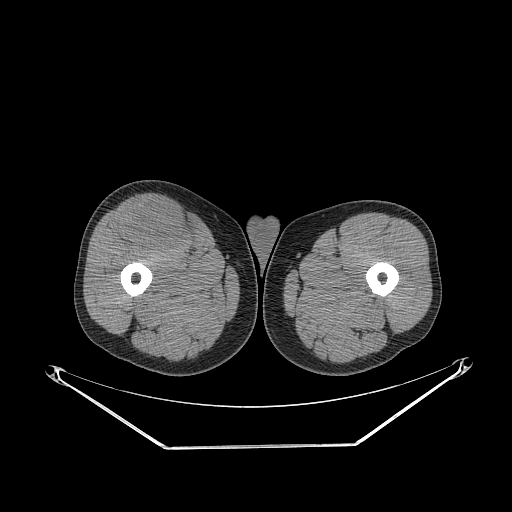
CT of an extremity soft-tissue mass (from a PET/CT study), one axial slice; slice 272 of 311 in the series (ordered by position); reconstruction kernel STANDARD; soft-tissue window (W 400 / L 40 HU); 3.75 mm slice thickness; 512 × 512 image matrix. Male patient. Case-level facts recorded for this patient, not image findings: histological type: pleiomorphic leiomyosarcoma; grade: intermediate; site of the primary tumour: right thigh.
Annotated regions visible in this slice (expert contour drawn on MRI and transferred to this co-registered scan by the dataset authors):
- gross tumour volume including surrounding oedema: bounding box [x1, y1, x2, y2] px = [119, 201, 186, 254]
- gross tumour volume (mass): [119, 203, 186, 254]